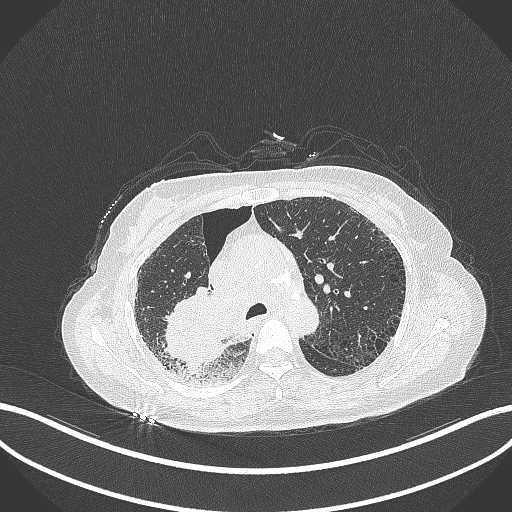
Chest CT, one axial slice. Position 234 of 408 along the scan axis. Reconstruction kernel B70f. Lung window (W 1500 / L -600 HU). 1 mm slice thickness. 512 × 512 image matrix, field of view 400 × 400 mm. Patient: female, 64 years. From the clinical record (not read from this slice): clinical TNM (as recorded): T3 N3 M0.
Structures marked on this image (bounding box drawn by a radiologist):
- lung tumour (recorded histology: squamous cell carcinoma): box from (x=162, y=285) to (x=233, y=372) px